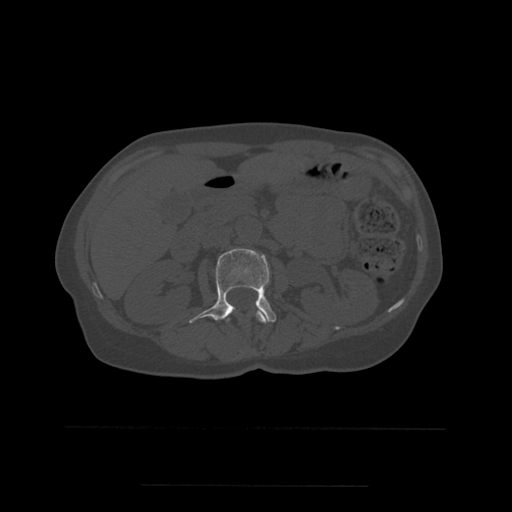
CT including the spine, one axial slice. Slice 218 of 544 in the series (ordered by position). Bone window (W 1800 / L 400 HU). 1.25 mm slice thickness. 512 × 512 image matrix, field of view 350 × 350 mm. Patient age 58 years. Case-level facts recorded for this patient, not image findings: primary cancer: lung.
Outlined on this slice (semi-automatically segmented with operator editing):
- L1 vertebra: bounding box (x1, y1, x2, y2) in pixels: (227, 310, 267, 324)
- L2 vertebra: (189, 249, 277, 323)